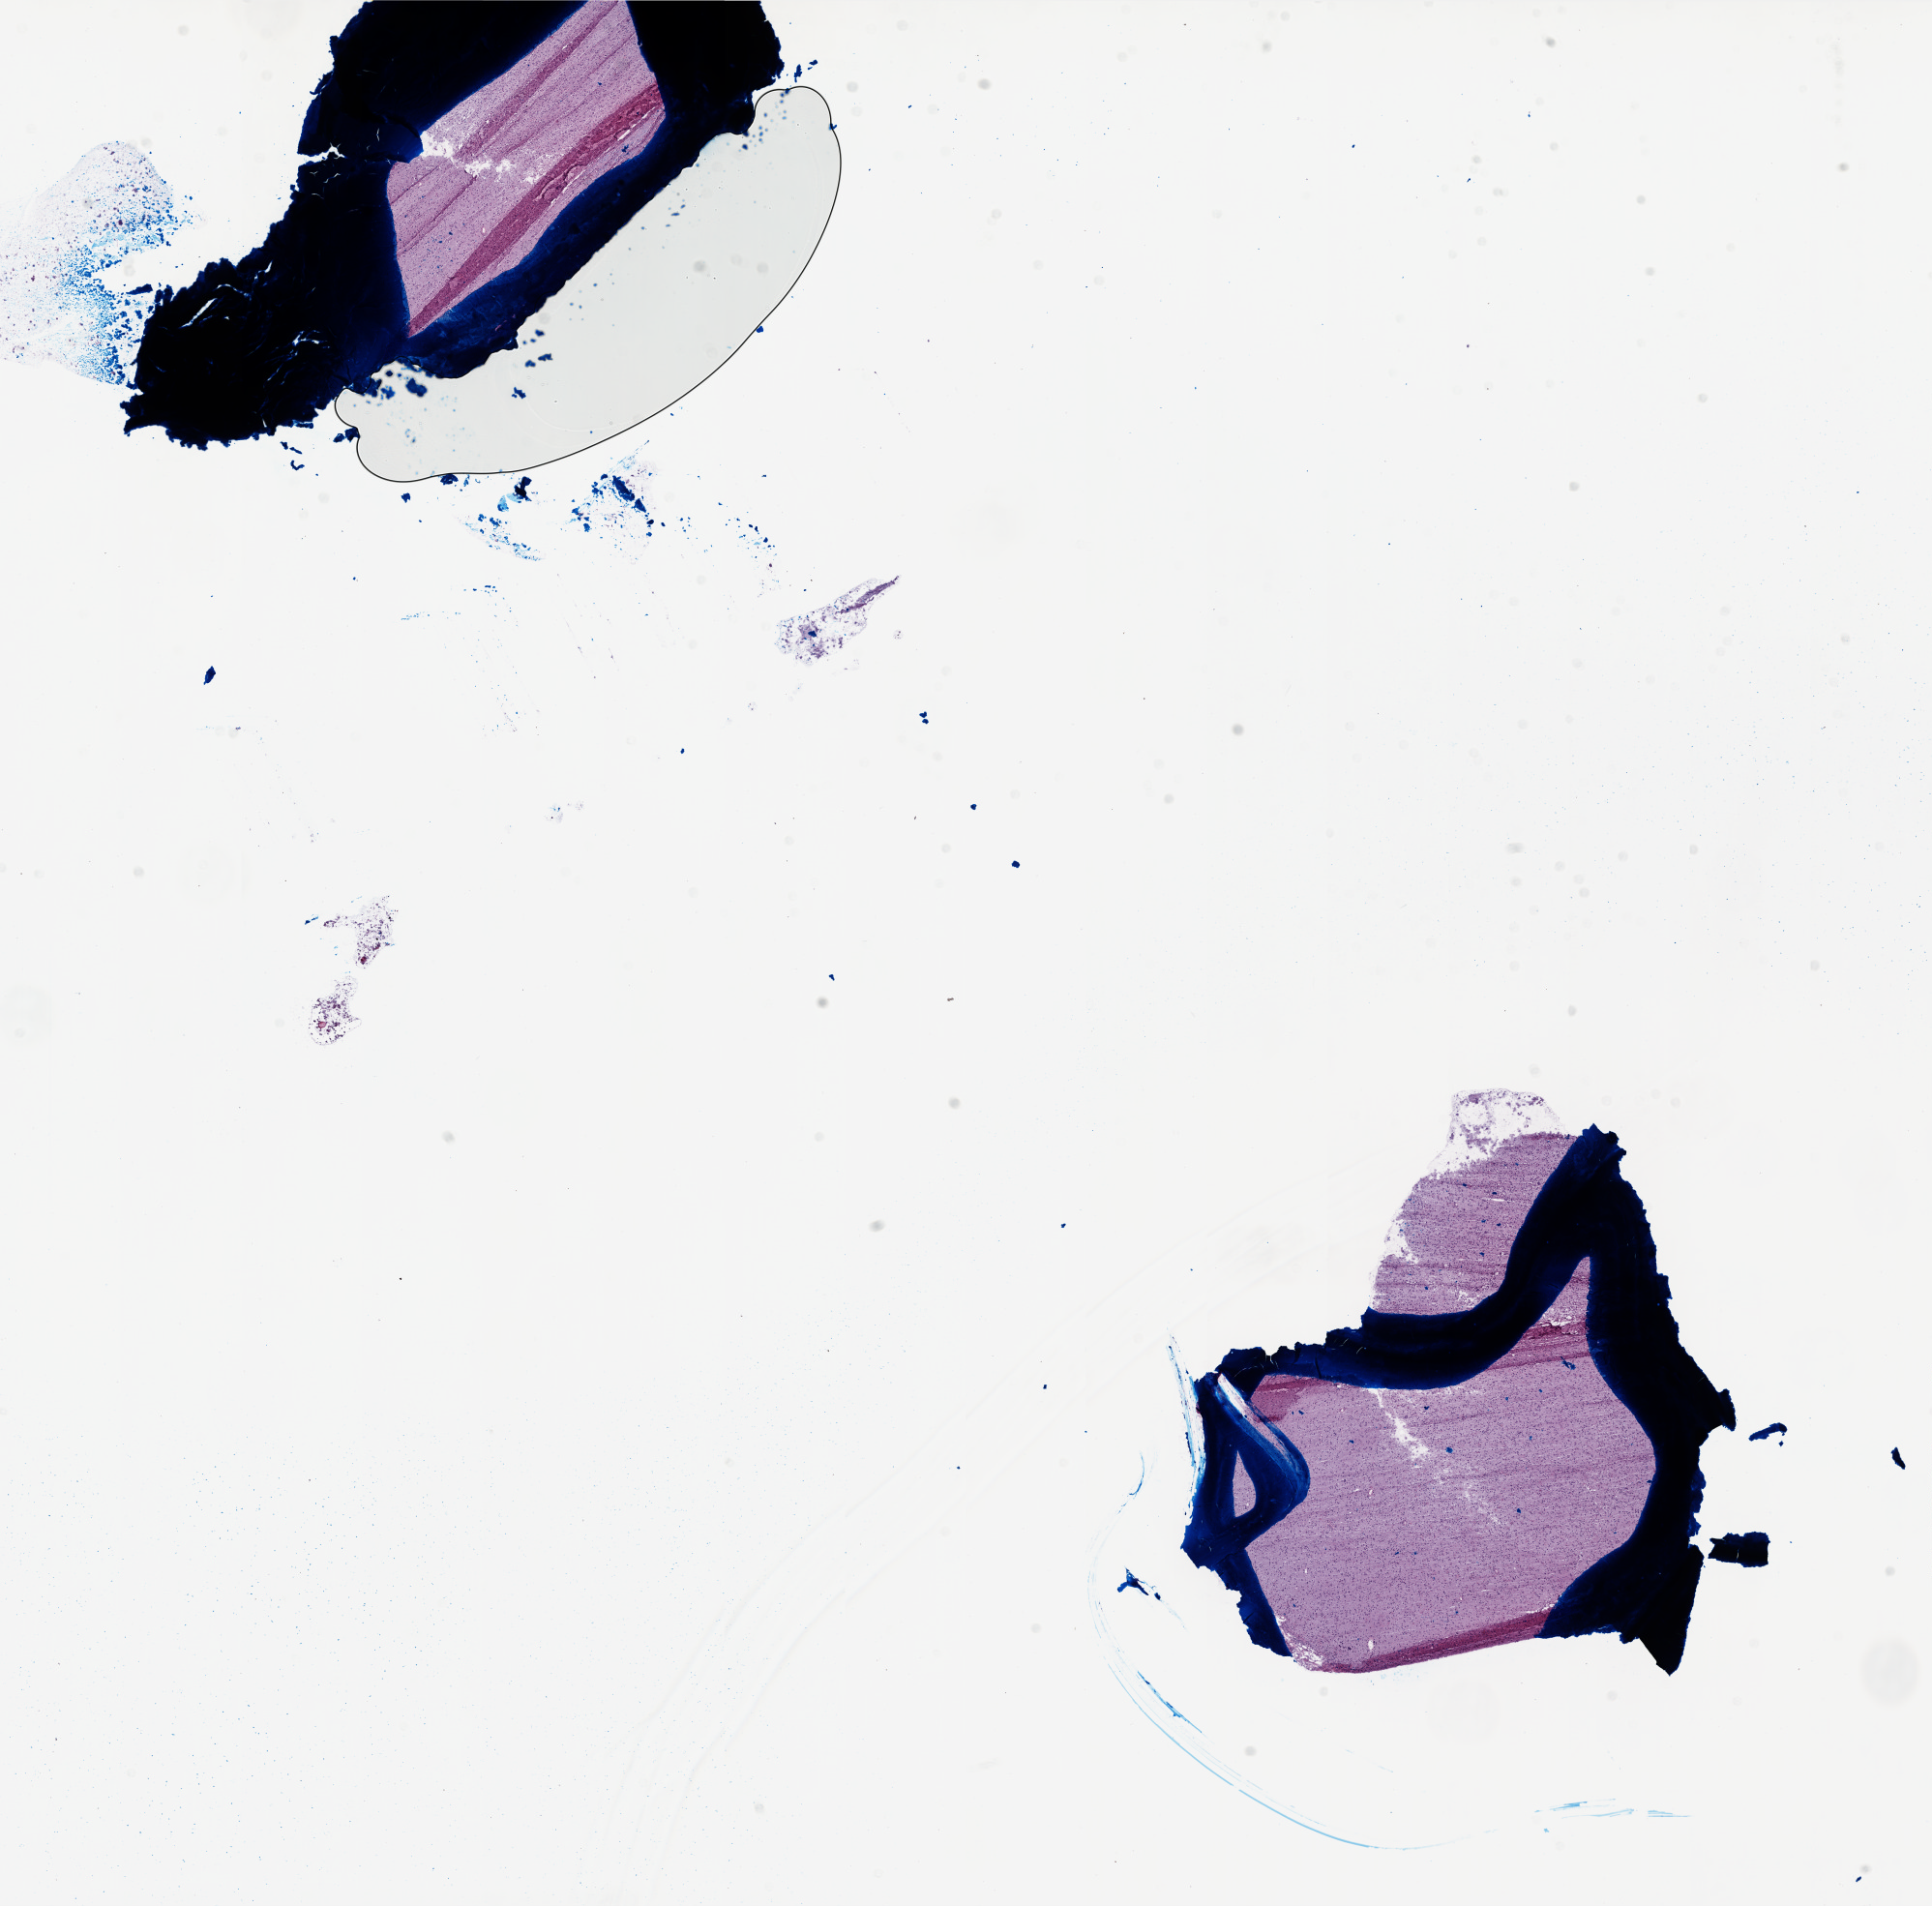
H&E-stained whole-slide image, a low-resolution overview of the entire scanned area, about 16.0 x 15.8 mm (acquisition: 20x scan), frozen section, sample: primary tumour, brain. Male, age 63 years at initial diagnosis. Pathologist review of this section (percent, as recorded): tumour cells 85%, tumour nuclei 85%, normal cells 0%, stromal cells 15%, necrosis 0%.
Histologic diagnosis: Glioblastoma.